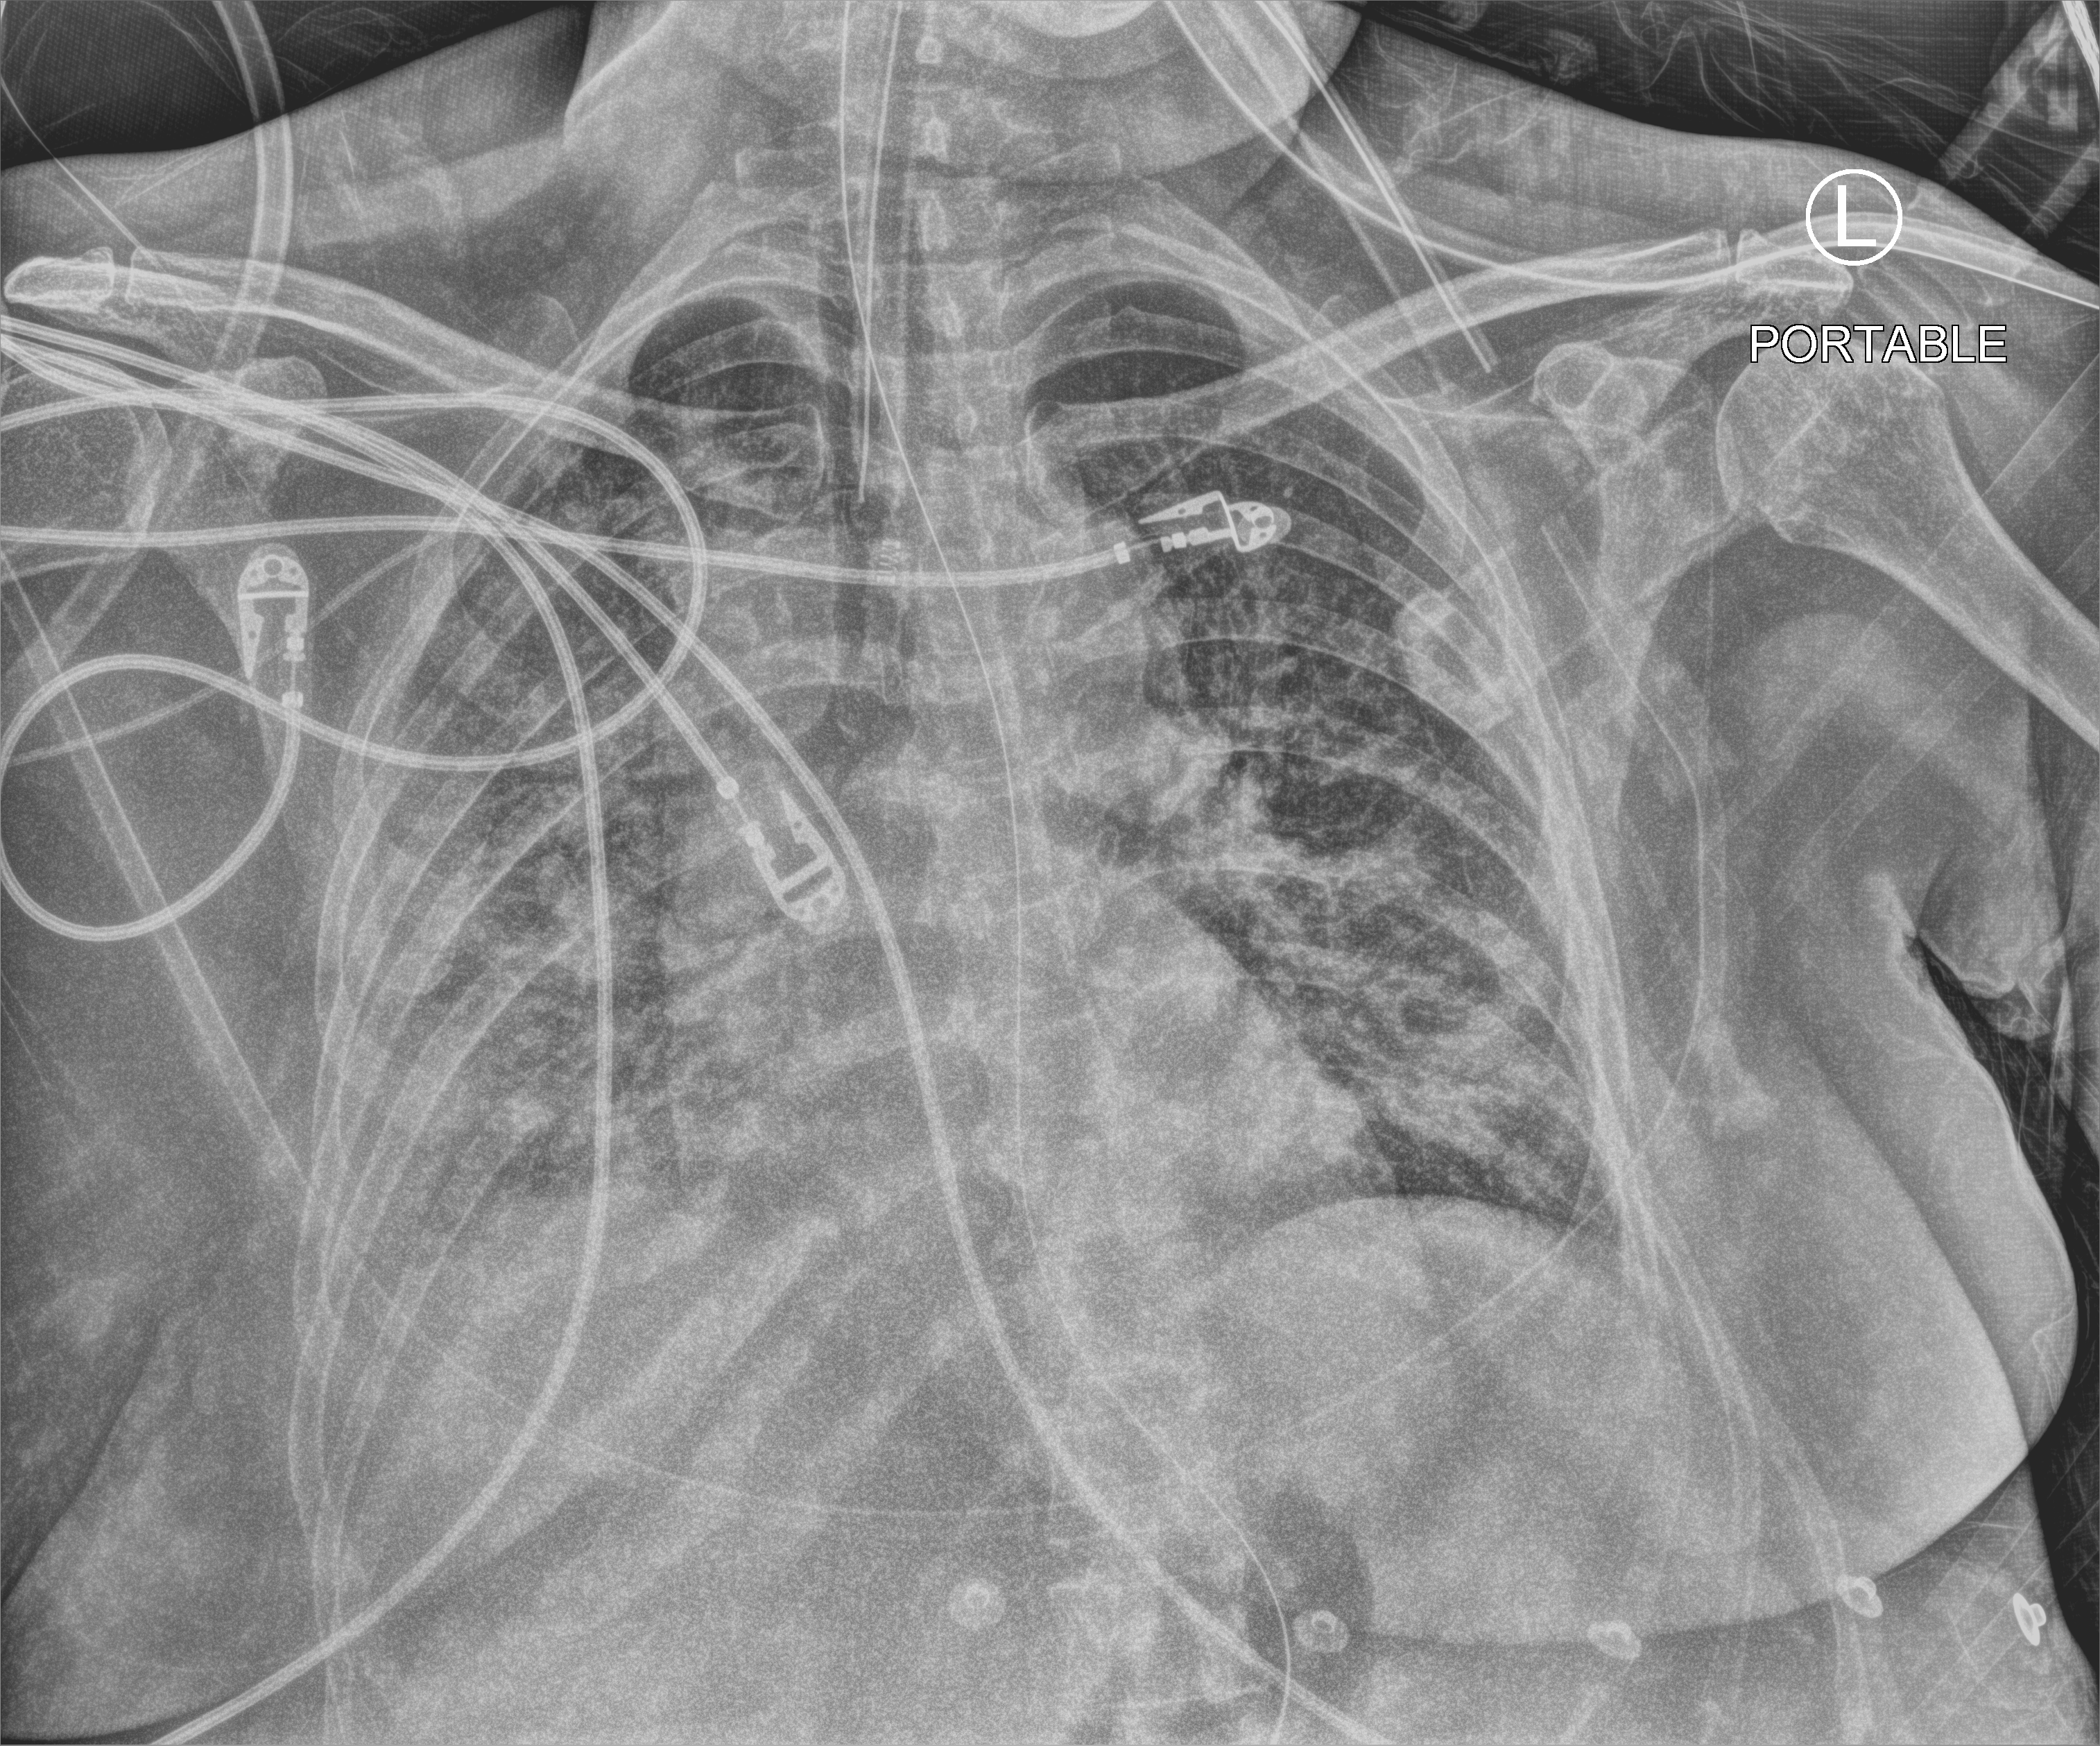
Chest X-ray (portable); anteroposterior (AP) projection. Patient hospitalised with COVID-19; female, aged 18–59 years.
Hospital-stay facts (about this admission, not read from this image; timing relative to this image not recorded): length of hospital stay: 22 days.